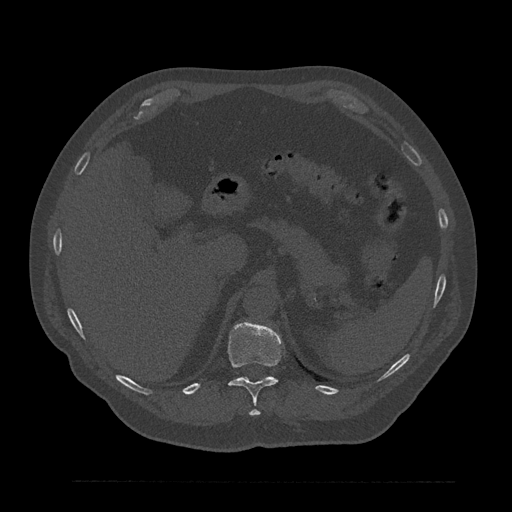
CT including the spine, one axial slice. Position 283 of 797 along the scan axis. Reconstruction kernel Br40s/3. 120 kVp. Bone window (W 1800 / L 400 HU). 0.5 mm slice thickness. 512 × 512 image matrix, field of view 430 × 430 mm. Male patient, age 61 years. Case-level facts recorded for this patient, not image findings: primary cancer: prostate.
Outlined on this slice (semi-automatic segmentation, software-assisted and operator-edited):
- T11 vertebra: bounding box <228,322,282,416> (left, top, right, bottom; pixels)